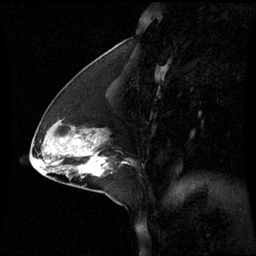
Breast MRI (dynamic contrast-enhanced), one sagittal slice. Position 26 of 60 along the scan axis. Dynamic contrast-enhanced series, image 2 of 3 at this slice position (ordered by acquisition). 1.5 T. TE 4.2 ms, TR 8.9 ms. 2.2 mm slice thickness. 256 × 256 image matrix. Female patient, age 44 years. From the clinical record (not read from this slice): setting: breast cancer imaged before/during neoadjuvant chemotherapy; receptor status: triple-negative.
Annotated regions visible in this slice (semi-automatic segmentation, software-assisted and operator-edited):
- analysis volume of interest (the breast-tissue region the enhancement analysis was run in; not a lesion): box from (x=76, y=150) to (x=105, y=179) px
- tumour enhancement mask (voxels above the 70 % enhancement threshold inside the analysis volume of interest): (x=90, y=158)–(x=105, y=177)